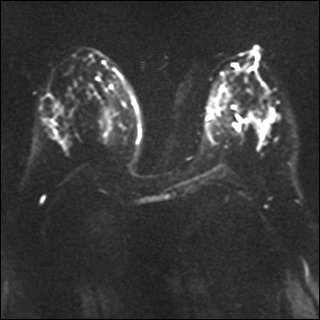
Breast MRI, one axial slice; position 17 of 41 along the scan axis; diffusion-weighted series; image 2 of 4 stored at this slice position (different b-values; order by instance number); 1.5 T; 4 mm slice thickness; 320 × 320 image matrix, field of view 340 × 340 mm. Female patient.
Outlined on this slice (expert manual segmentation):
- tumour on diffusion-weighted imaging: bounding box [x1, y1, x2, y2] px = [266, 112, 276, 122]